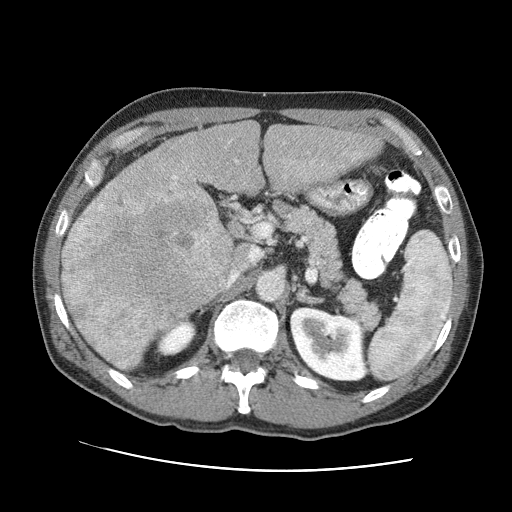
Contrast-enhanced abdominal CT (liver protocol), one axial slice. Slice 44 of 95 in the series (ordered by position). 120 kVp. One of 2 acquisitions stored at this slice position. Soft-tissue window (W 400 / L 40 HU). 2.5 mm slice thickness. 512 × 512 image matrix, field of view 360 × 360 mm. From the clinical record (not read from this slice): diagnosis: hepatocellular carcinoma (patient treated with transarterial chemoembolisation; whether this scan precedes or follows treatment is not stated here); TNM stage (as recorded): Stage-IVA; Child-Pugh class: A; tumour differentiation: moderately differentiated.
Outlined on this slice (semi-automatically segmented with operator editing):
- liver parenchyma outside the tumour (the mass and vessels are separate outlines, so this box may not span the whole liver): bounding box (x1, y1, x2, y2) in pixels: (88, 120, 382, 321)
- mass: (60, 171, 236, 365)
- liver vessels: (162, 139, 361, 178)